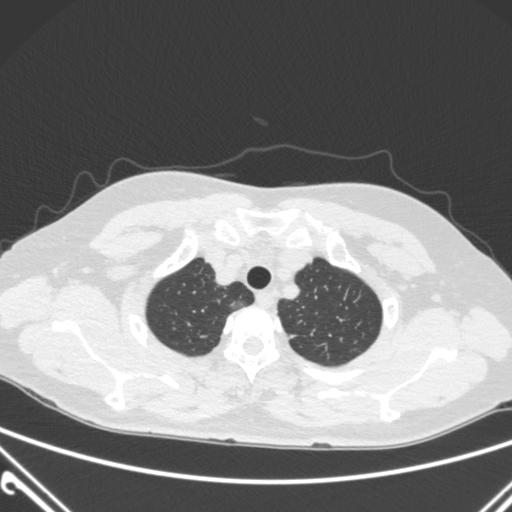
Chest CT, one axial slice; position 247 of 300 along the scan axis; 120 kVp; lung window (W 1500 / L -600 HU); 1 mm slice thickness; 512 × 512 image matrix, field of view 350 × 350 mm. Patient: female, 54 years. From the clinical record (not read from this slice): clinical TNM (as recorded): T1a N0 M0.
Outlined on this slice (bounding box drawn by a radiologist):
- lung tumour (recorded histology: adenocarcinoma): bounding box (x1, y1, x2, y2) in pixels: (228, 294, 255, 319)